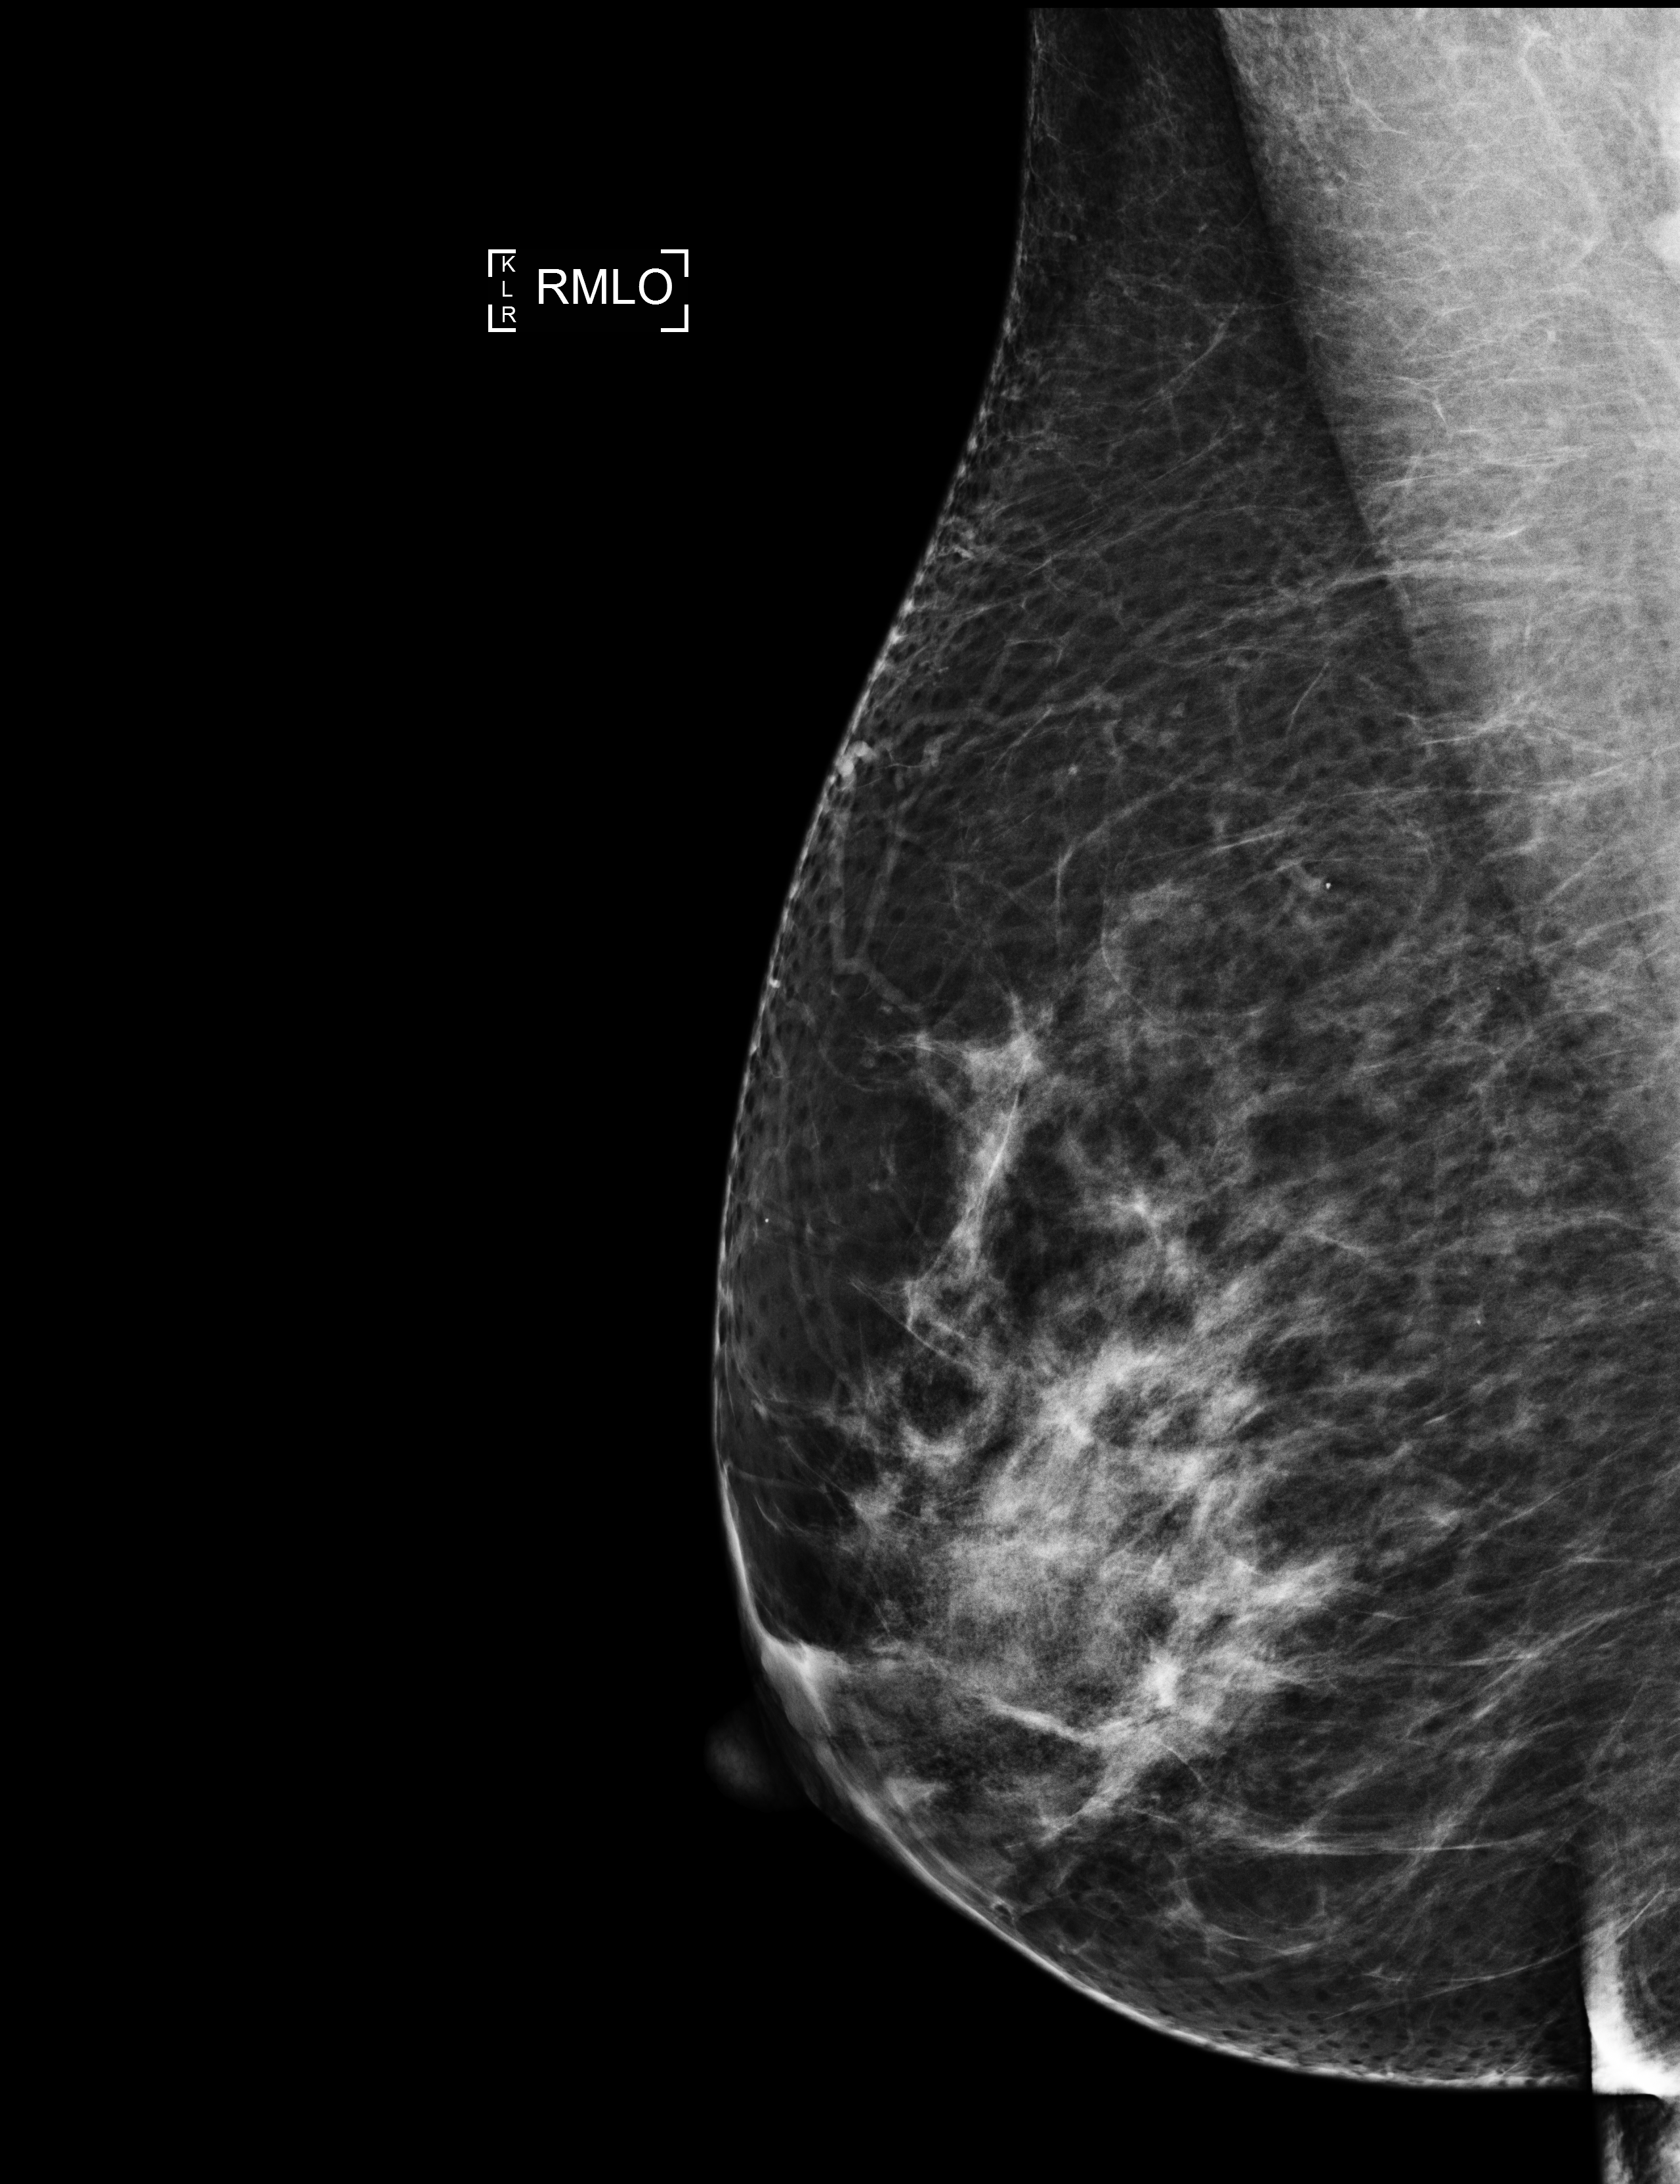
Annual screening mammography examination; compressed breast thickness 83 mm; system: Selenia Dimensions. Female patient, age 51 years.
Image type: full-field digital mammogram. Breast: right. Projection: mediolateral oblique (MLO) view.